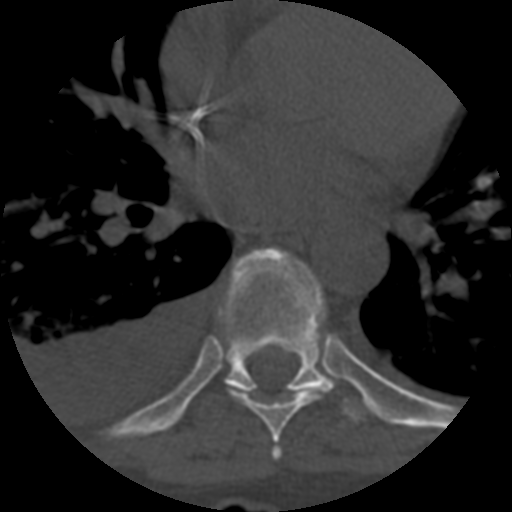
CT including the spine, one axial slice; position 406 of 708 along the scan axis; reconstruction kernel STANDARD; 120 kVp; one of 3 acquisitions stored at this slice position; bone window (W 1800 / L 400 HU); 512 × 512 image matrix. Patient age 55 years. Case-level facts recorded for this patient, not image findings: primary cancer: colon.
Outlined on this slice (semi-automatic segmentation, software-assisted and operator-edited):
- T6 vertebra: bounding box [x1, y1, x2, y2] px = [272, 448, 280, 459]
- T7 vertebra: [230, 380, 333, 448]
- T8 vertebra: [217, 248, 373, 423]